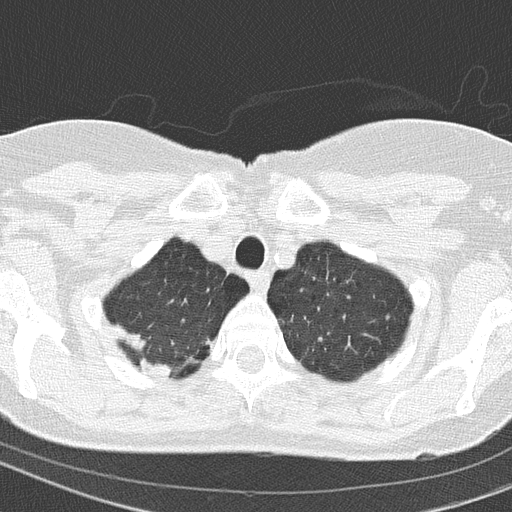
Low-dose screening chest CT, axial slice; baseline screening round; lung window (W 1500 / L -600 HU); 2 mm slice thickness; slice 19 of 154 in the series. Female participant, aged 67 years at enrolment.
• Expert reader's lesion annotation, bounding box <125,339,189,388> (left, top, right, bottom; pixels).
• The exam's reader record, not a measurement of the box and not confirmed to be the same lesion: non-calcified nodule or mass ≥4 mm, right upper lobe, 15 × 14 mm, spiculated (stellate) margins, soft tissue attenuation.
• Official screen result: positive, change unspecified: nodule(s) >= 4 mm or enlarging nodule(s), mass(es), or other non-specific abnormalities suspicious for lung cancer.
• Lung cancer was diagnosed 63 days after this screen: adenocarcinoma, NOS, right upper lobe, moderately differentiated (G2), stage IA (AJCC 6th edition), 14 mm at pathology.